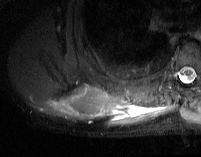
MRI of an extremity soft-tissue mass, one axial slice; slice 16 of 74 in the series (ordered by position); STIR; MR volume resampled by the dataset authors to the PET/CT grid (not the native acquisition matrix); 201 × 157 image matrix, field of view 196 × 153 mm. Male patient. From the clinical record (not read from this slice): histological type: pleiomorphic spindle cell undifferentiated; grade: high; site of the primary tumour: right parascapusular.
Annotated regions visible in this slice (expert contour drawn on MRI and transferred to this co-registered scan by the dataset authors):
- gross tumour volume including surrounding oedema: bounding box [x1, y1, x2, y2] px = [42, 86, 171, 126]